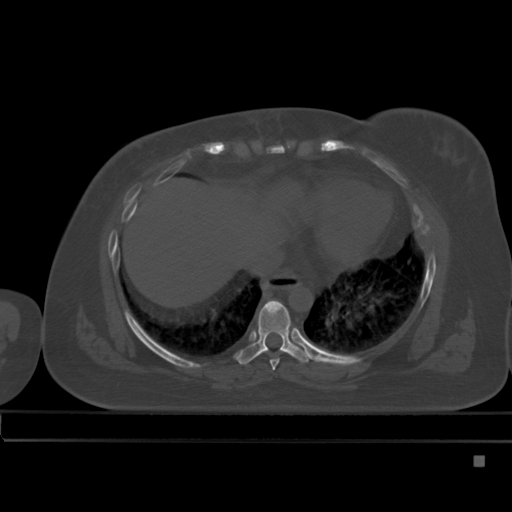
CT including the spine, one axial slice. Position 281 of 495 along the scan axis. Bone window (W 1800 / L 400 HU). 512 × 512 image matrix. Female patient, age 33 years. From the clinical record (not read from this slice): primary cancer: breast.
Annotated regions visible in this slice (semi-automatically segmented with operator editing):
- T7 vertebra: box from (x=270, y=336) to (x=292, y=370) px
- T8 vertebra: (x=235, y=300)–(x=311, y=365)